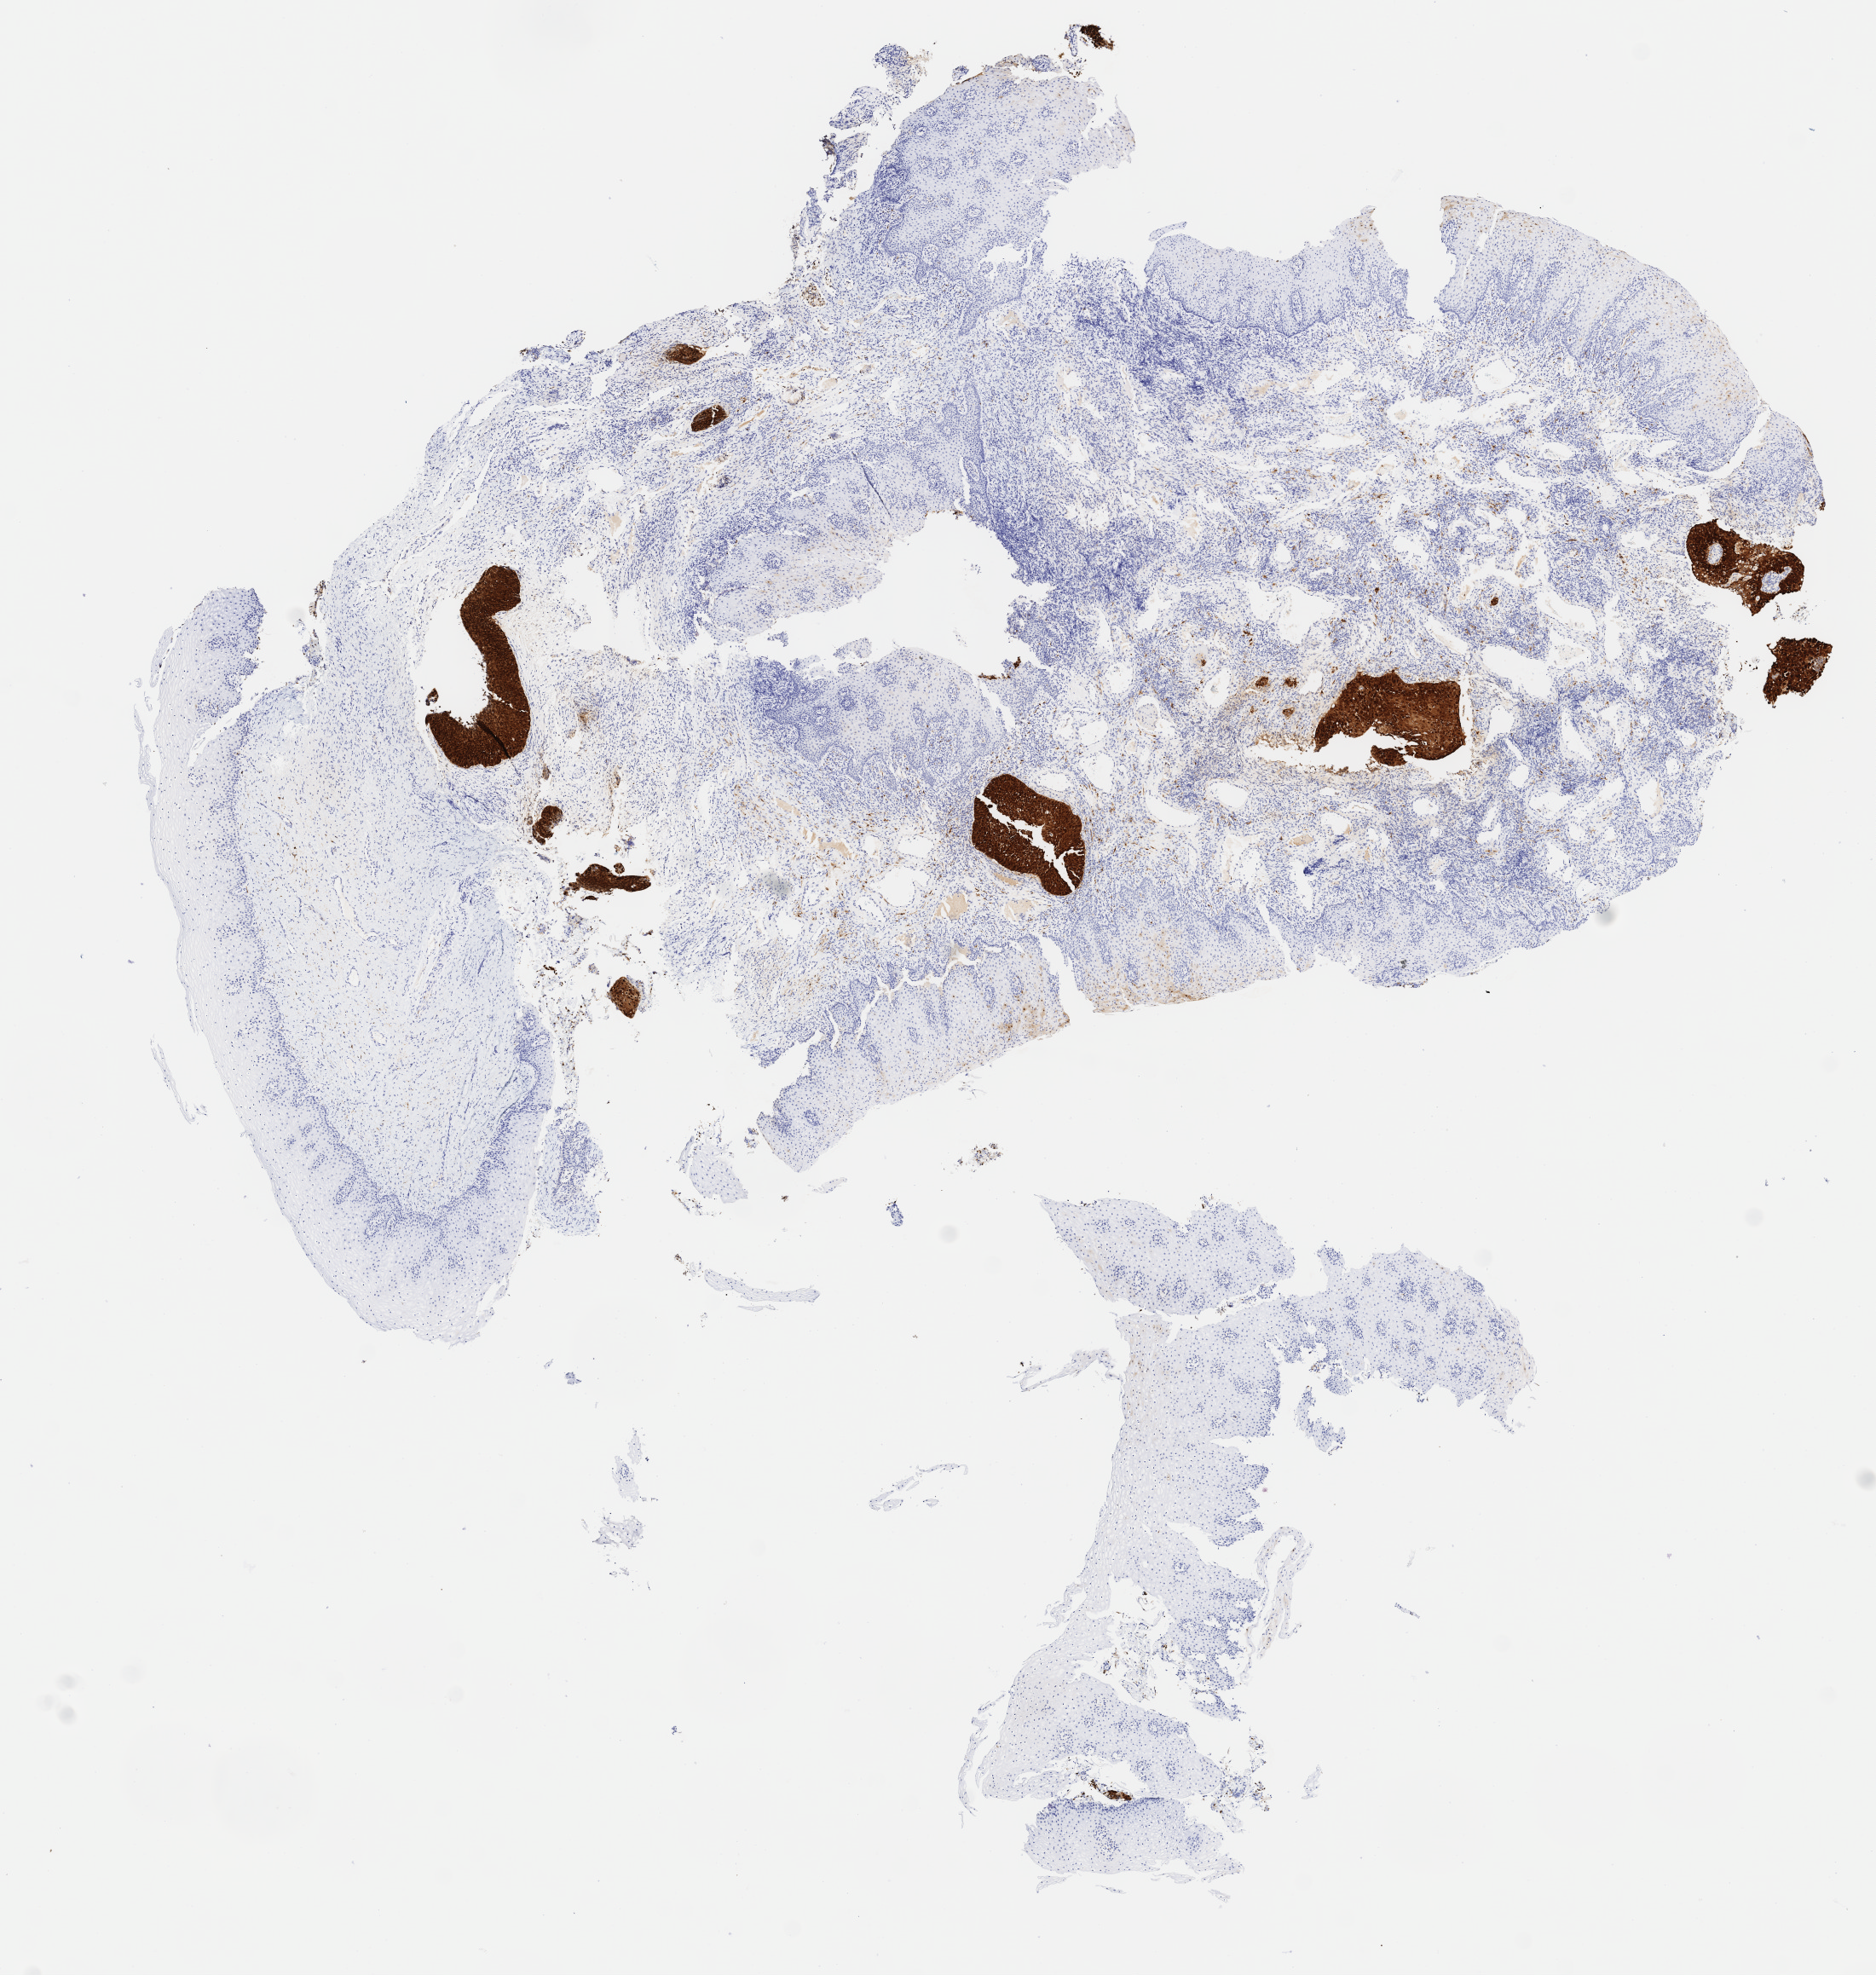
IHC for p16 (p16INK4a), whole-slide image — whole scanned area (about 8.8 x 9.2 mm) shown as a low-resolution overview; specimen: tumor tissue; anatomic site: cervix. Patient female; aged 47.
Histologic diagnosis: Squamous cell carcinoma, large cell, nonkeratinizing, NOS.